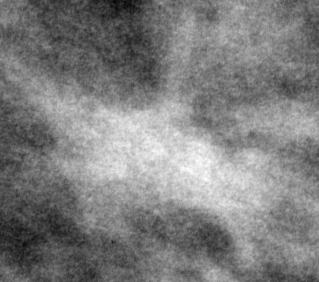
Region of interest cut from a scanned film mammogram (one marked finding), right breast, MLO view.
Mass, shape irregular, margins spiculated; BI-RADS assessment category 4; pathology (as recorded): malignant.